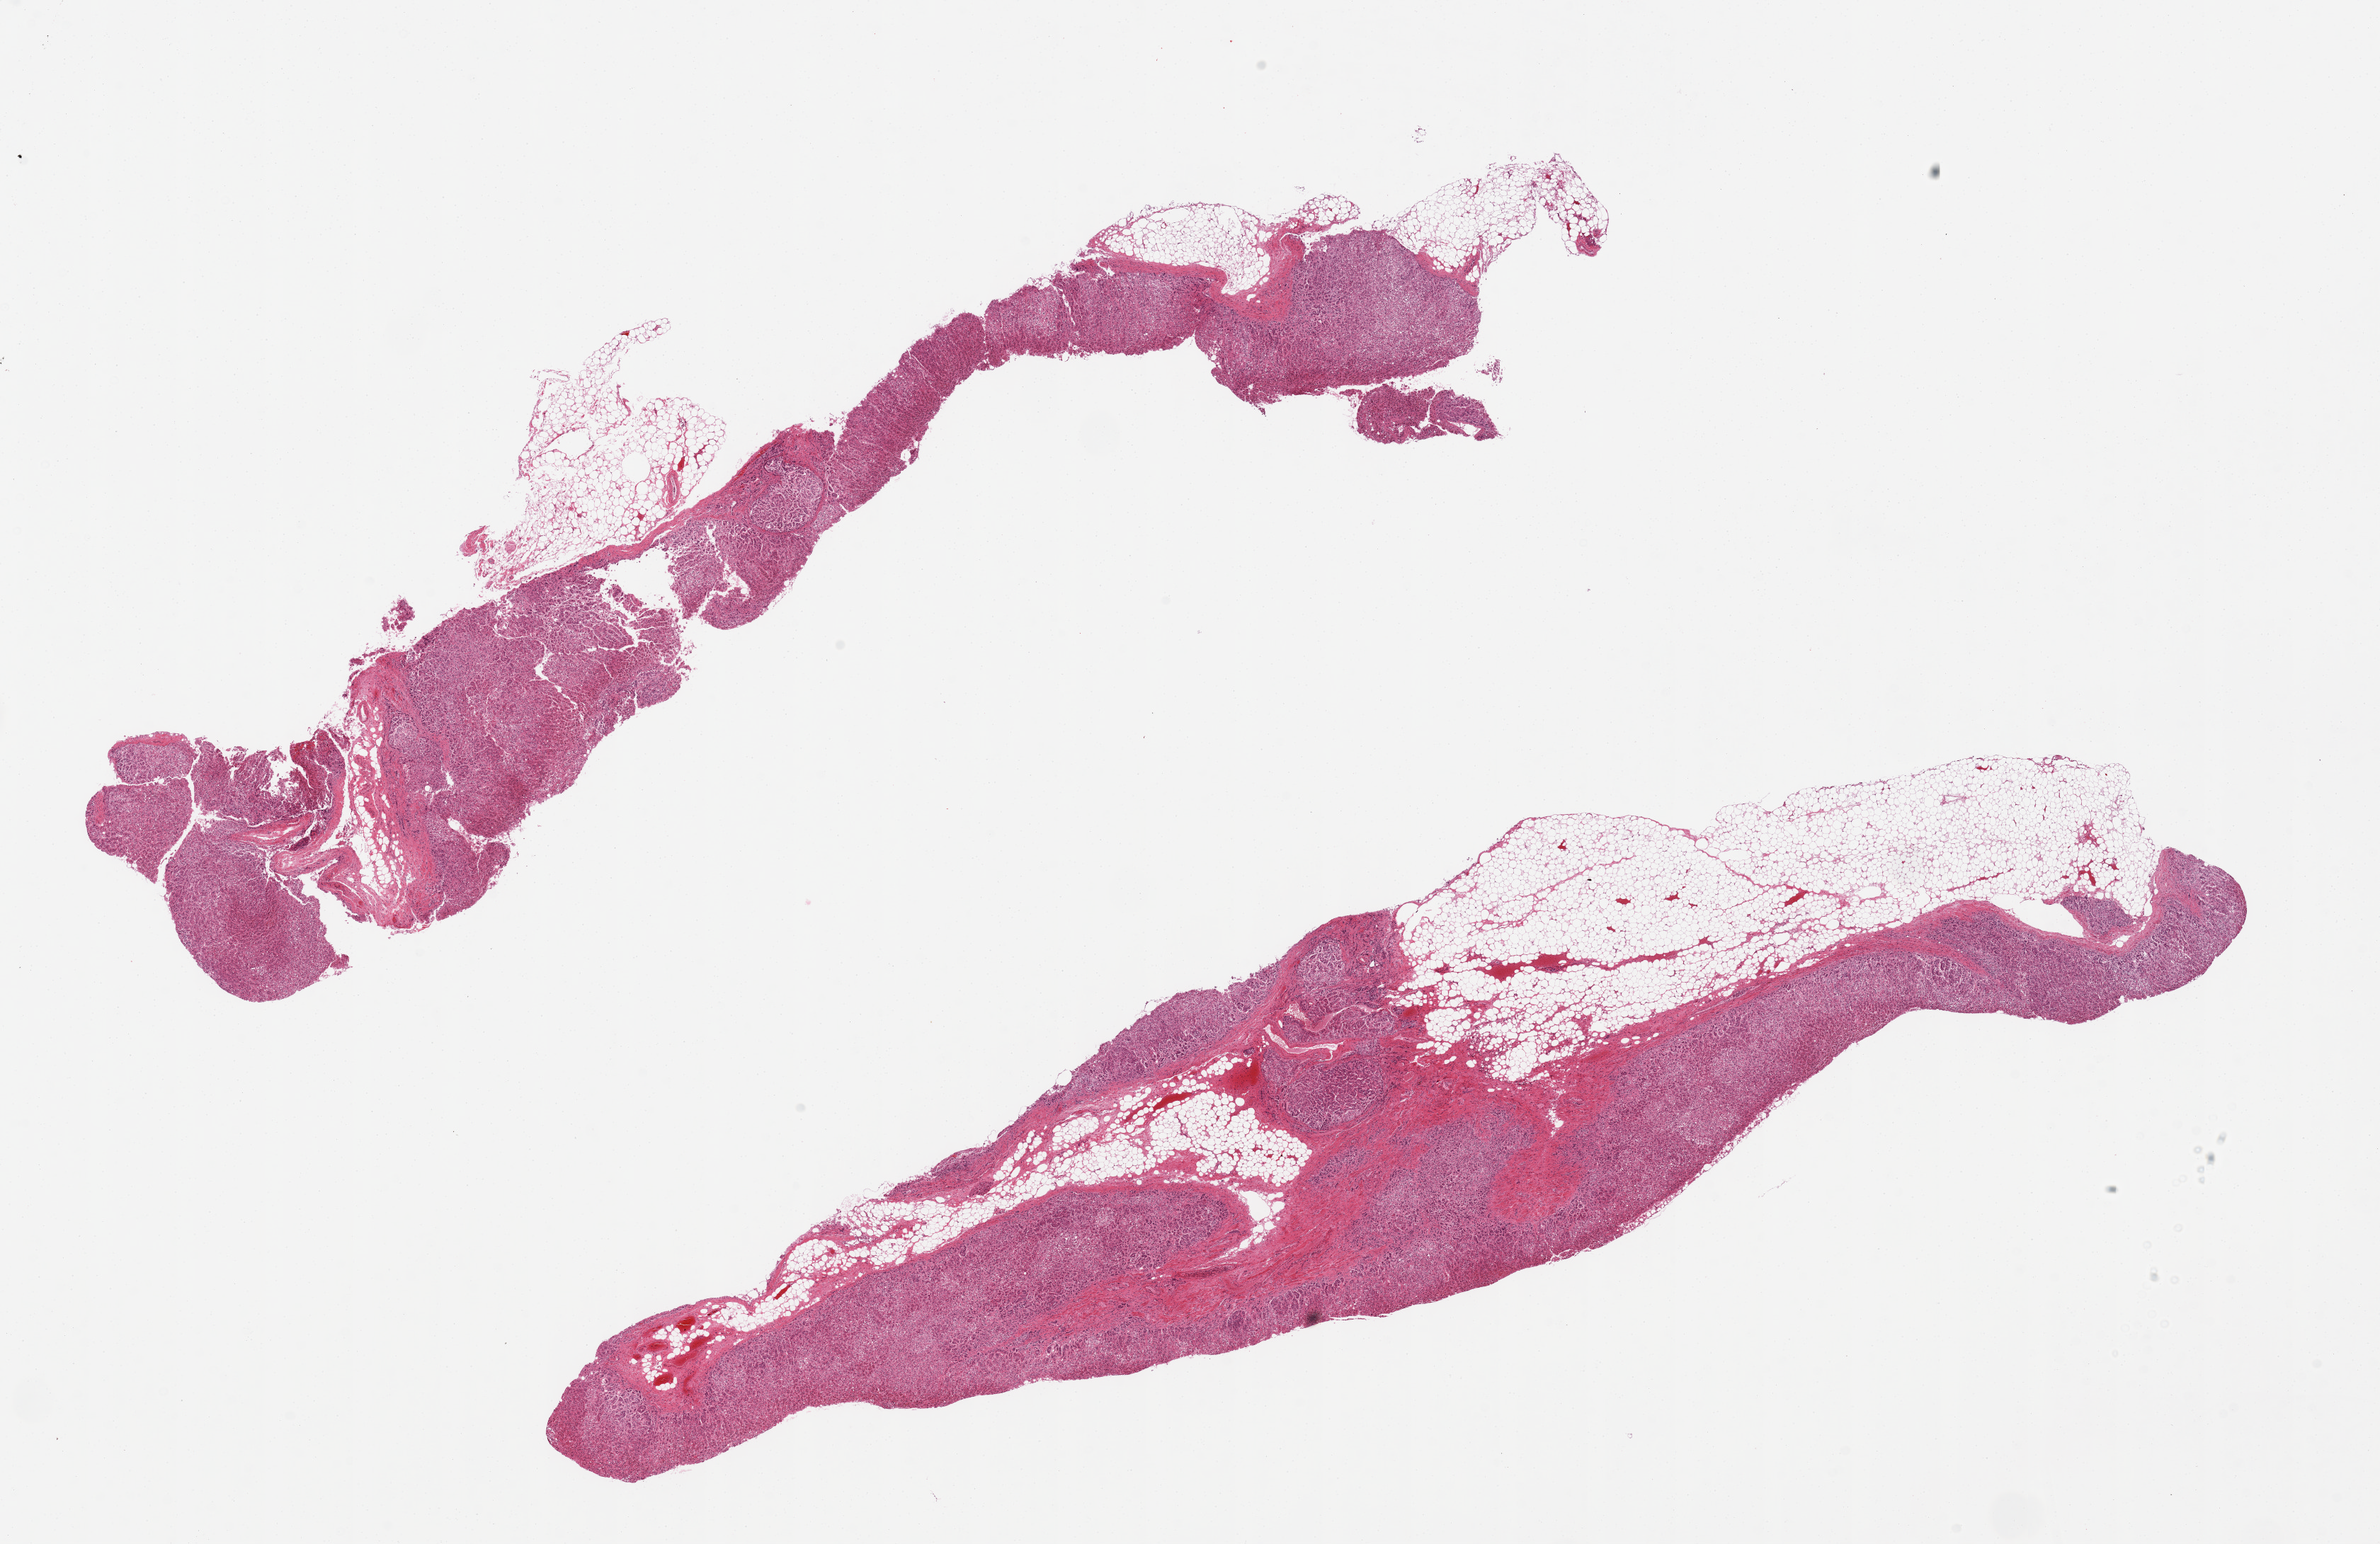
H&E whole-slide image — a low-resolution overview of the entire scanned area, about 26.6 x 17.2 mm. PAXgene-fixed paraffin-embedded (PFPE) section. Target tissue: adrenal gland. Donor tissue sample. Male donor.
Reviewer comment on this tissue sample: 2 pieces; 40 & 20% internal & external fat.